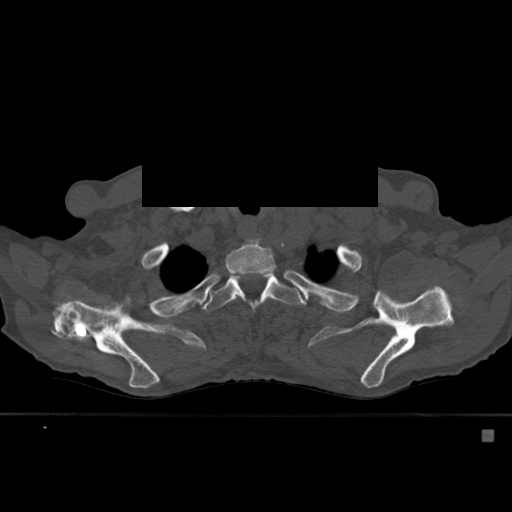
CT including the spine, one axial slice. Position 438 of 527 along the scan axis. Bone window (W 1800 / L 400 HU). 1.5 mm slice thickness. 512 × 512 image matrix, field of view 373 × 373 mm. Patient: male, 78 years. From the clinical record (not read from this slice): primary cancer: prostate.
Structures marked on this image (semi-automatically segmented with operator editing):
- T2 vertebra: bounding box [x1, y1, x2, y2] px = [225, 241, 276, 295]
- T3 vertebra: [202, 274, 303, 314]